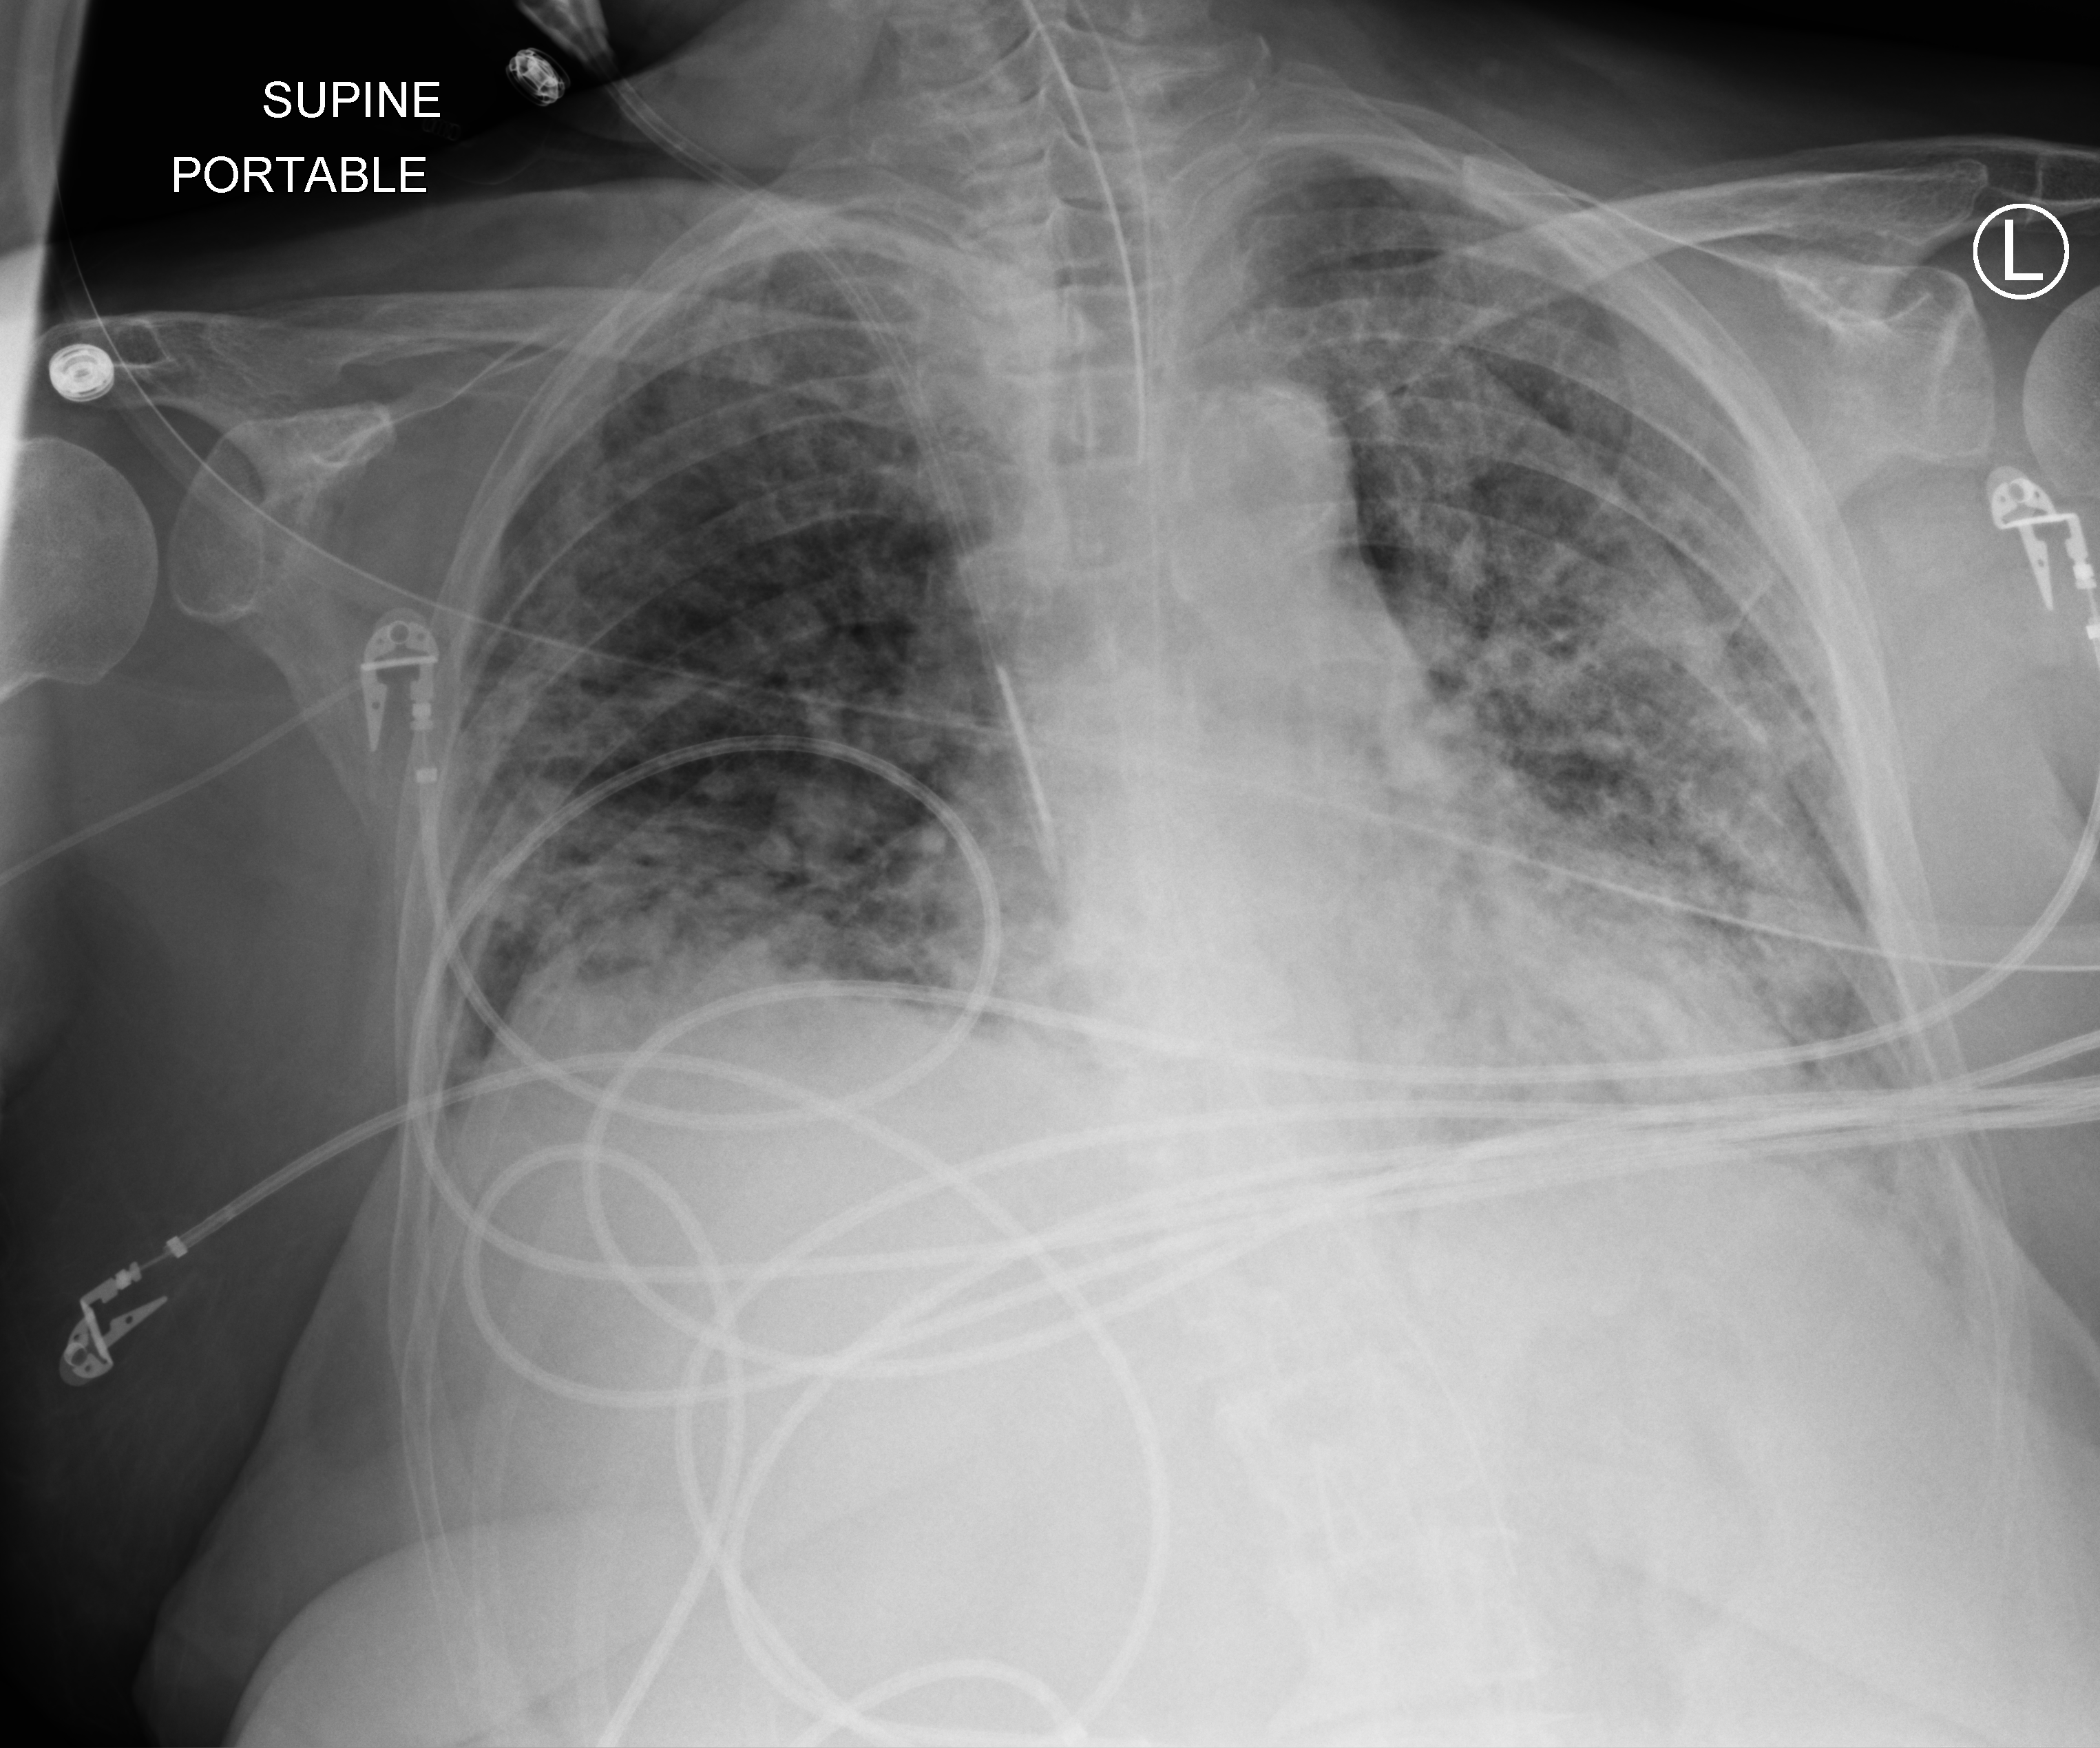
Portable chest radiograph; anteroposterior (AP) projection. Female patient hospitalised with COVID-19, age 75–90 years.
From the hospital-stay record, not from the radiograph (when in the stay this image was taken is not recorded):
- length of hospital stay: 28 days
- mechanically ventilated during this hospital stay: yes